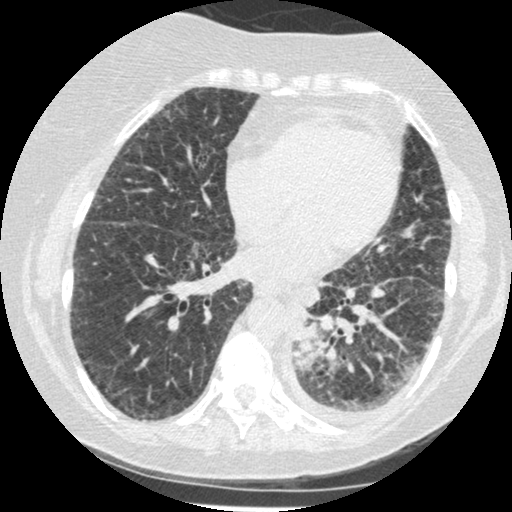
Low-dose screening chest CT, one axial slice. Slice 80 of 341 in the series (ordered by position). Reconstruction kernel STANDARD. Lung window (W 1500 / L -600 HU). 1.25 mm slice thickness. 512 × 512 image matrix.
Outlined on this slice (outlined manually by an expert reader):
- lesion 1 (tumor, lower lobe of left lung): bounding box [x1, y1, x2, y2] px = [293, 326, 321, 351]